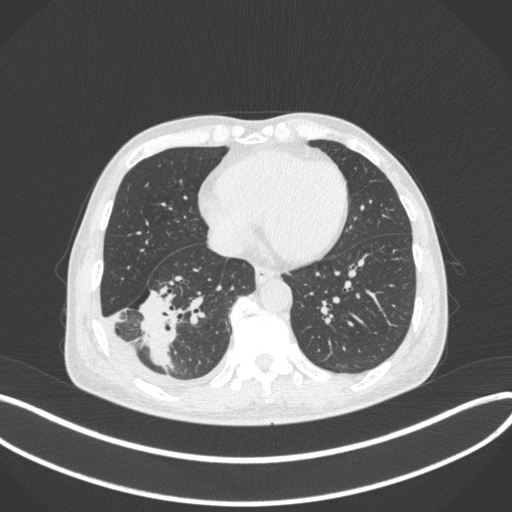
Chest CT, one axial slice. Slice 129 of 385 in the series (ordered by position). Reconstruction kernel B31f. 120 kVp. Lung window (W 1500 / L -600 HU). 1 mm slice thickness. 512 × 512 image matrix, field of view 400 × 400 mm. Patient: male, 64 years. From the clinical record (not read from this slice): clinical TNM (as recorded): T3 N0 M0; histopathological grade: G2-3.
Annotated regions visible in this slice (bounding box drawn by a radiologist):
- lung tumour (recorded histology: adenocarcinoma): bounding box [x1, y1, x2, y2] px = [131, 286, 180, 375]